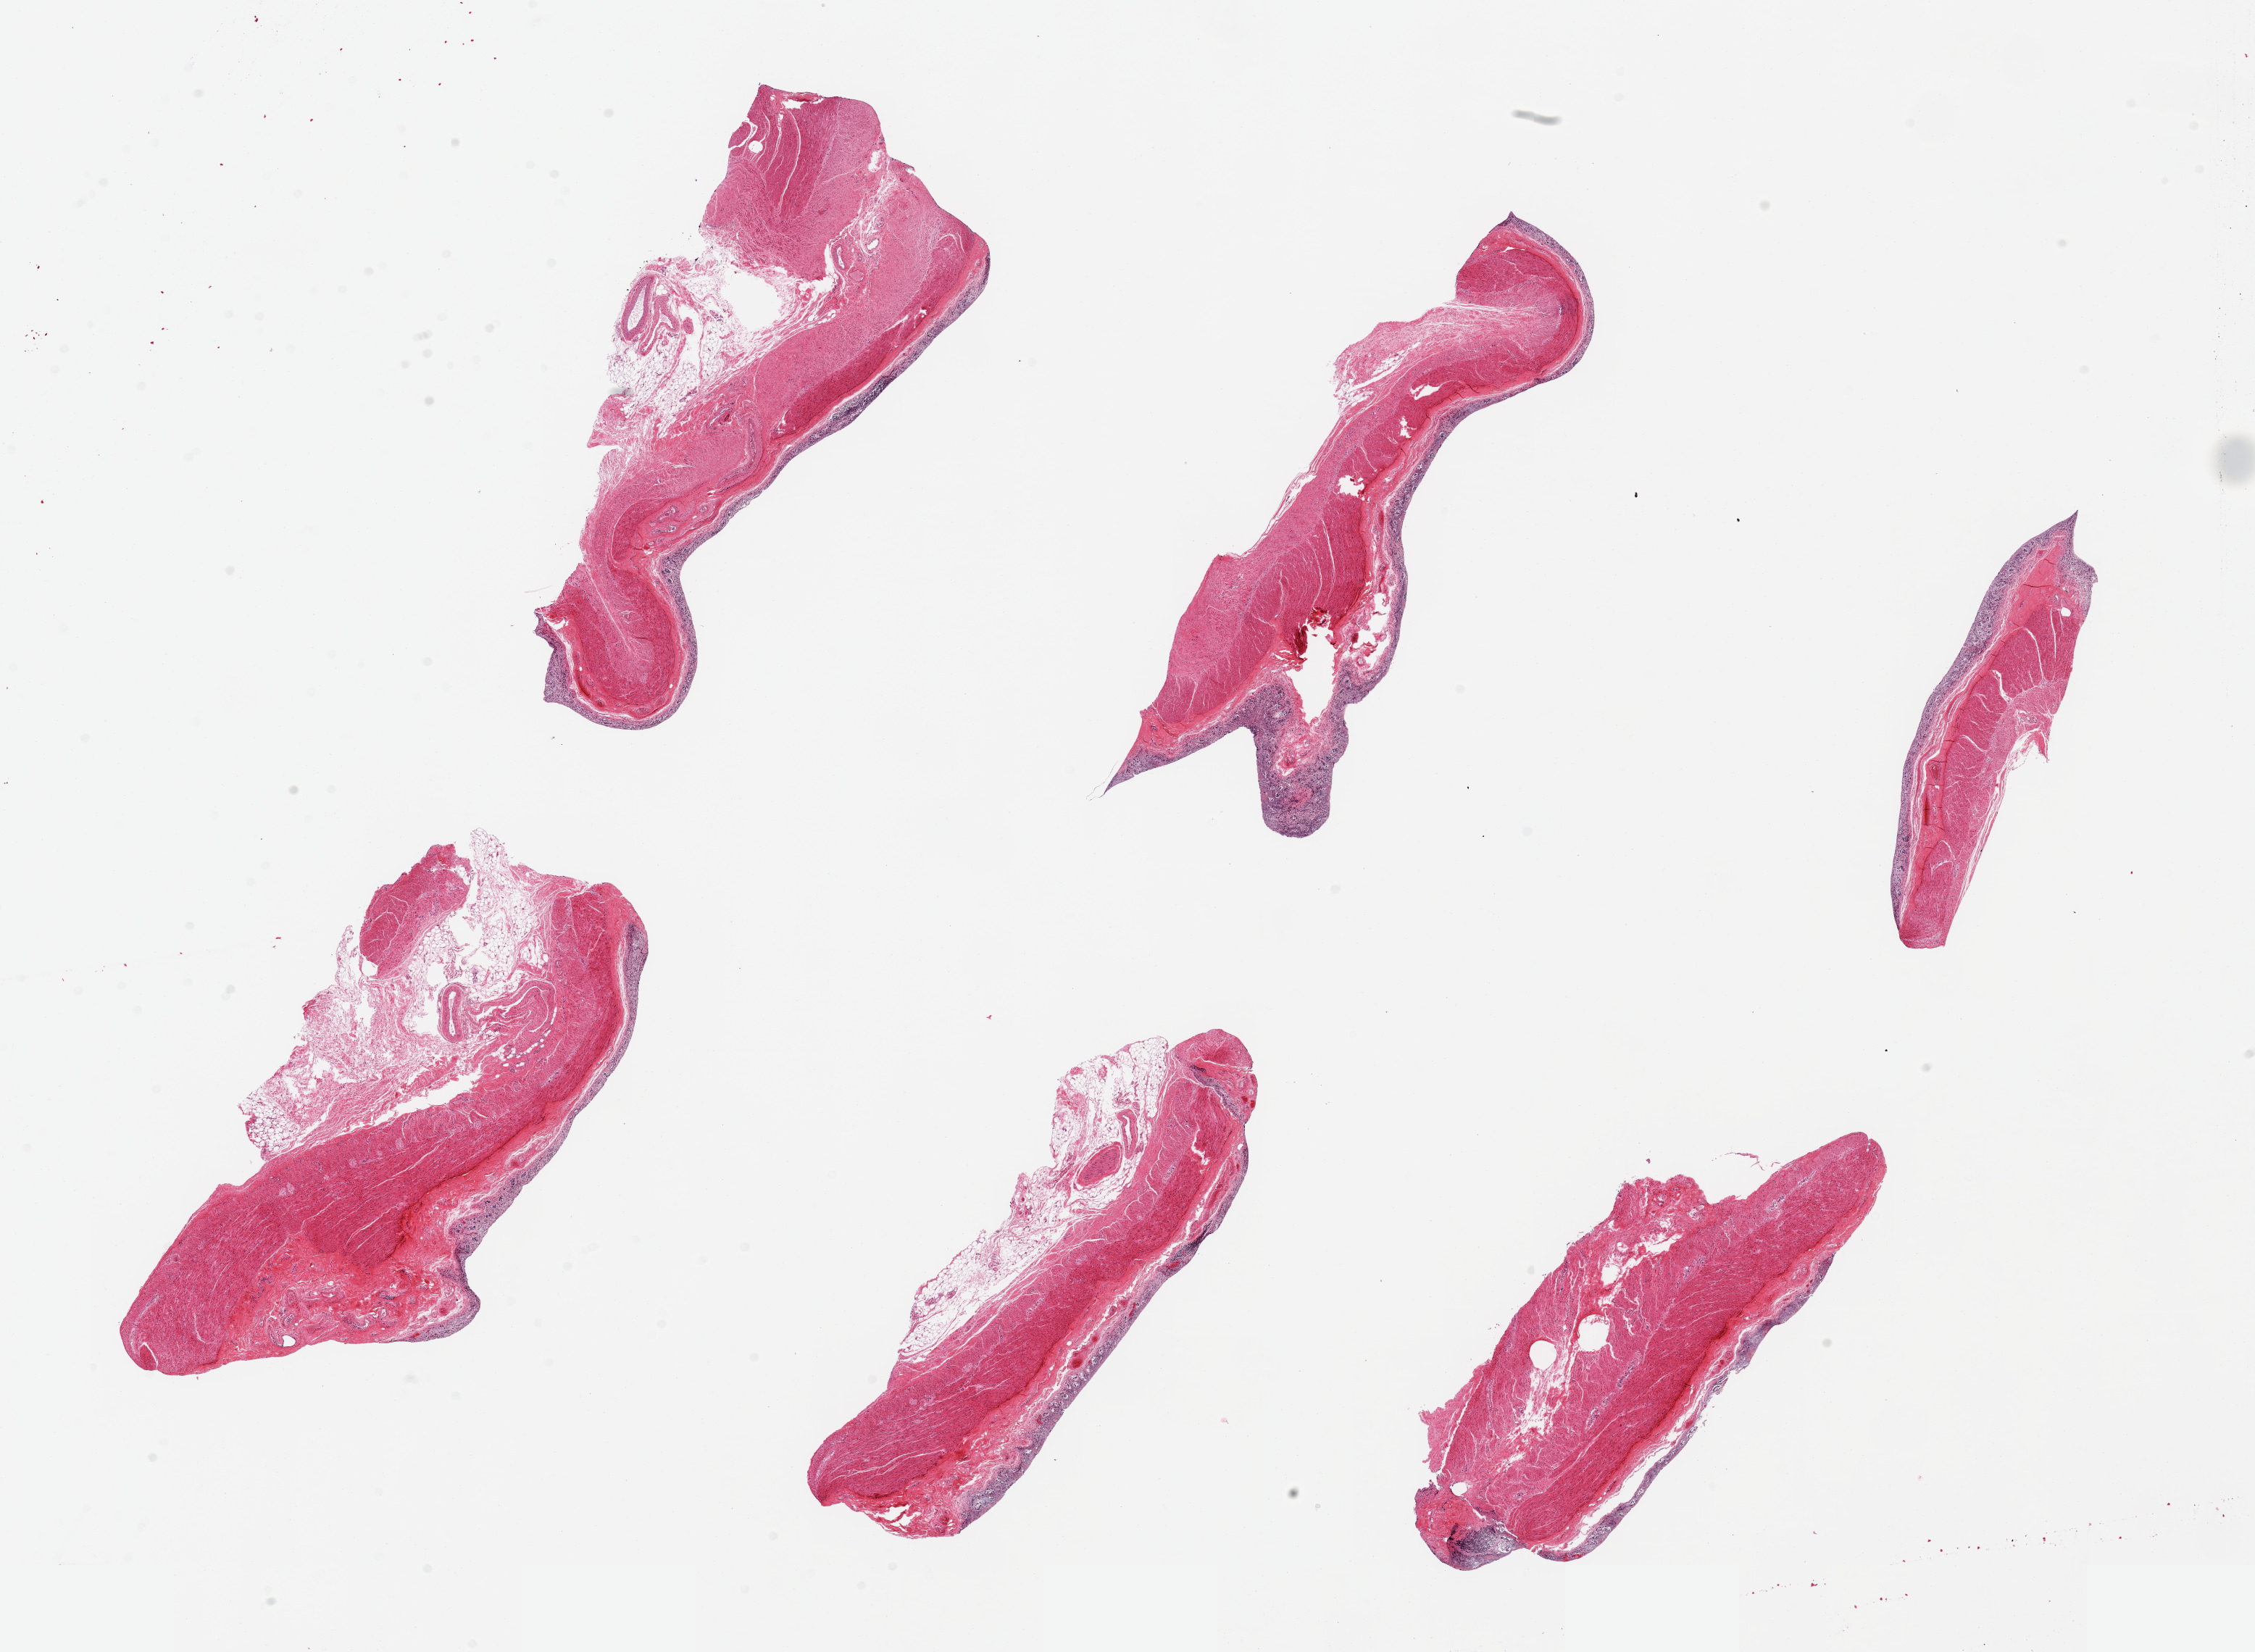
Whole-slide image, H&E stain, a low-resolution overview of the entire scanned area, about 24.6 x 18.0 mm (acquisition: 20x scan); PAXgene-fixed, paraffin-embedded tissue; target tissue: transverse colon; donor tissue sample. Donor sex: male.
* reviewer comment on this tissue sample: 6 pieces, up to 7x3mm; Glands = 3; muscle = 2